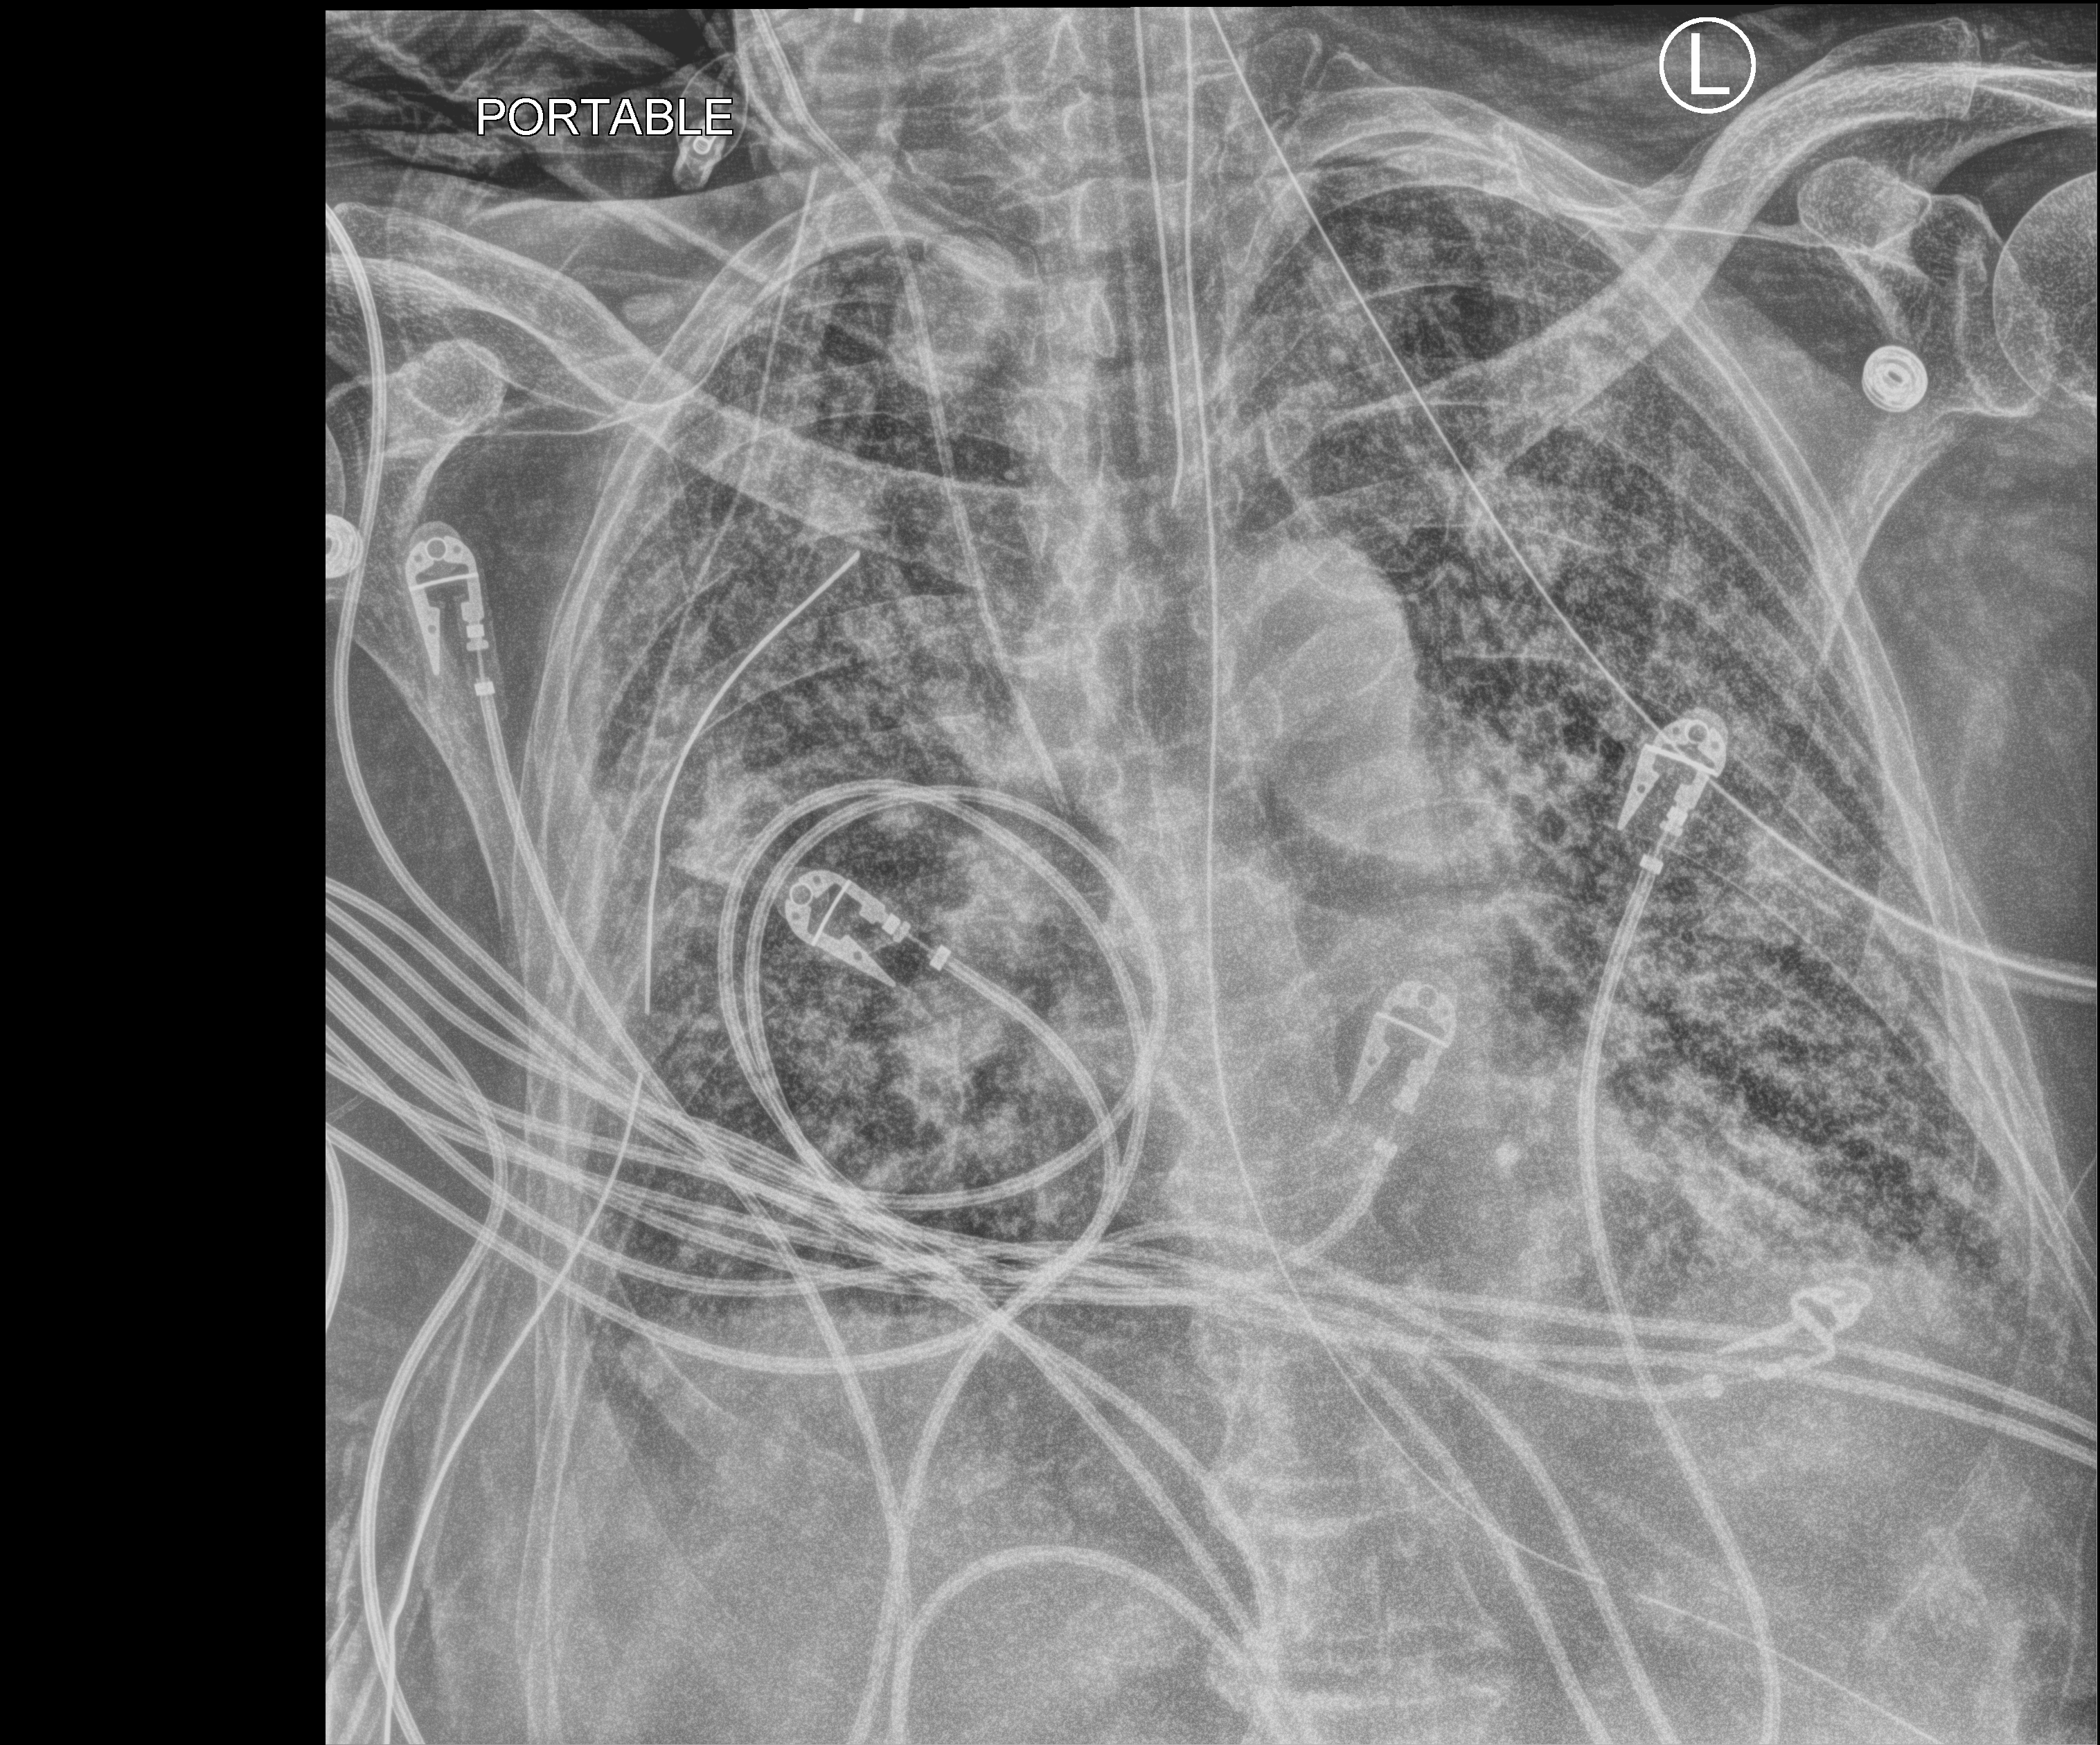
Bedside chest radiograph (computed radiography); anteroposterior (AP) projection. Patient hospitalised with COVID-19; male, aged 75–90 years.
Hospital-stay facts (about this admission, not read from this image; timing relative to this image not recorded):
- admitted to intensive care during this hospital stay: yes
- mechanically ventilated during this hospital stay: yes
- length of hospital stay: 47 days